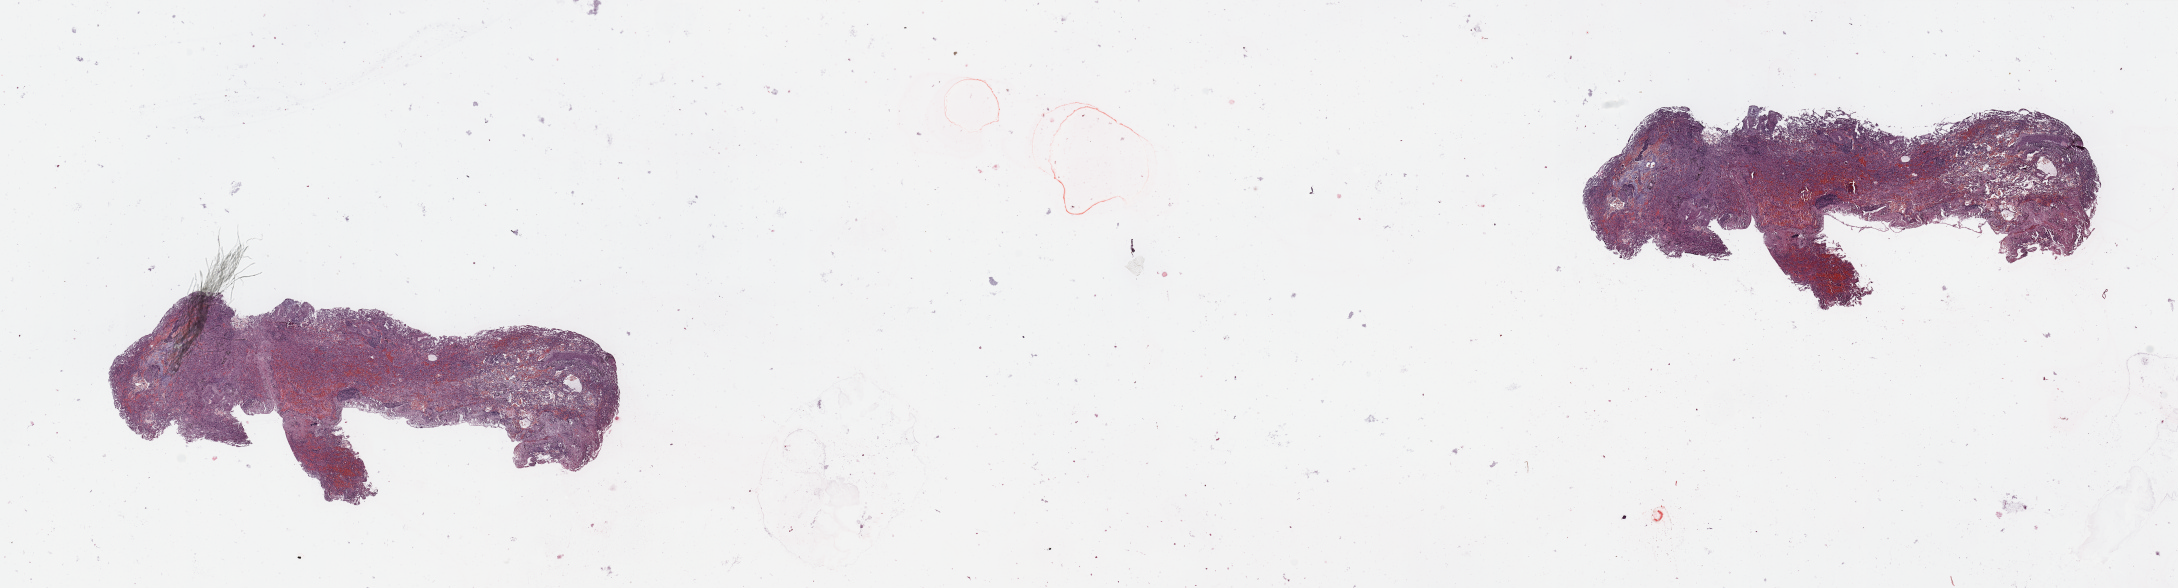
Whole-slide histology image, H&E-stained, low-resolution overview of the scanned area, about 34.5 x 9.3 mm (slide scanned at 20x), normal (non-tumour) tissue sample, lung. 55-year-old male patient.
• this section: normal (non-tumour) tissue from the same patient
• patient diagnosis: Adenocarcinoma, NOS